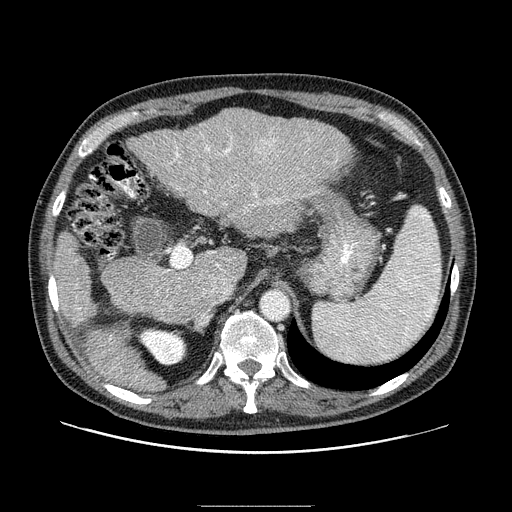
Contrast-enhanced abdominal CT (liver protocol), one axial slice. Slice 54 of 99 in the series (ordered by position). One of 2 acquisitions stored at this slice position. Soft-tissue window (W 400 / L 40 HU). 2.5 mm slice thickness. 512 × 512 image matrix, field of view 400 × 400 mm. From the clinical record (not read from this slice): diagnosis: hepatocellular carcinoma (patient treated with transarterial chemoembolisation; whether this scan precedes or follows treatment is not stated here); TNM stage (as recorded): Stage-II; Child-Pugh class: A; tumour differentiation: well differentiated; tumour nodularity: multinodular.
Structures marked on this image (semi-automatic segmentation, software-assisted and operator-edited):
- liver parenchyma outside the tumour (the mass and vessels are separate outlines, so this box may not span the whole liver): bounding box [x1, y1, x2, y2] px = [52, 108, 351, 384]
- mass: [253, 137, 279, 160]
- liver vessels: [79, 137, 311, 310]